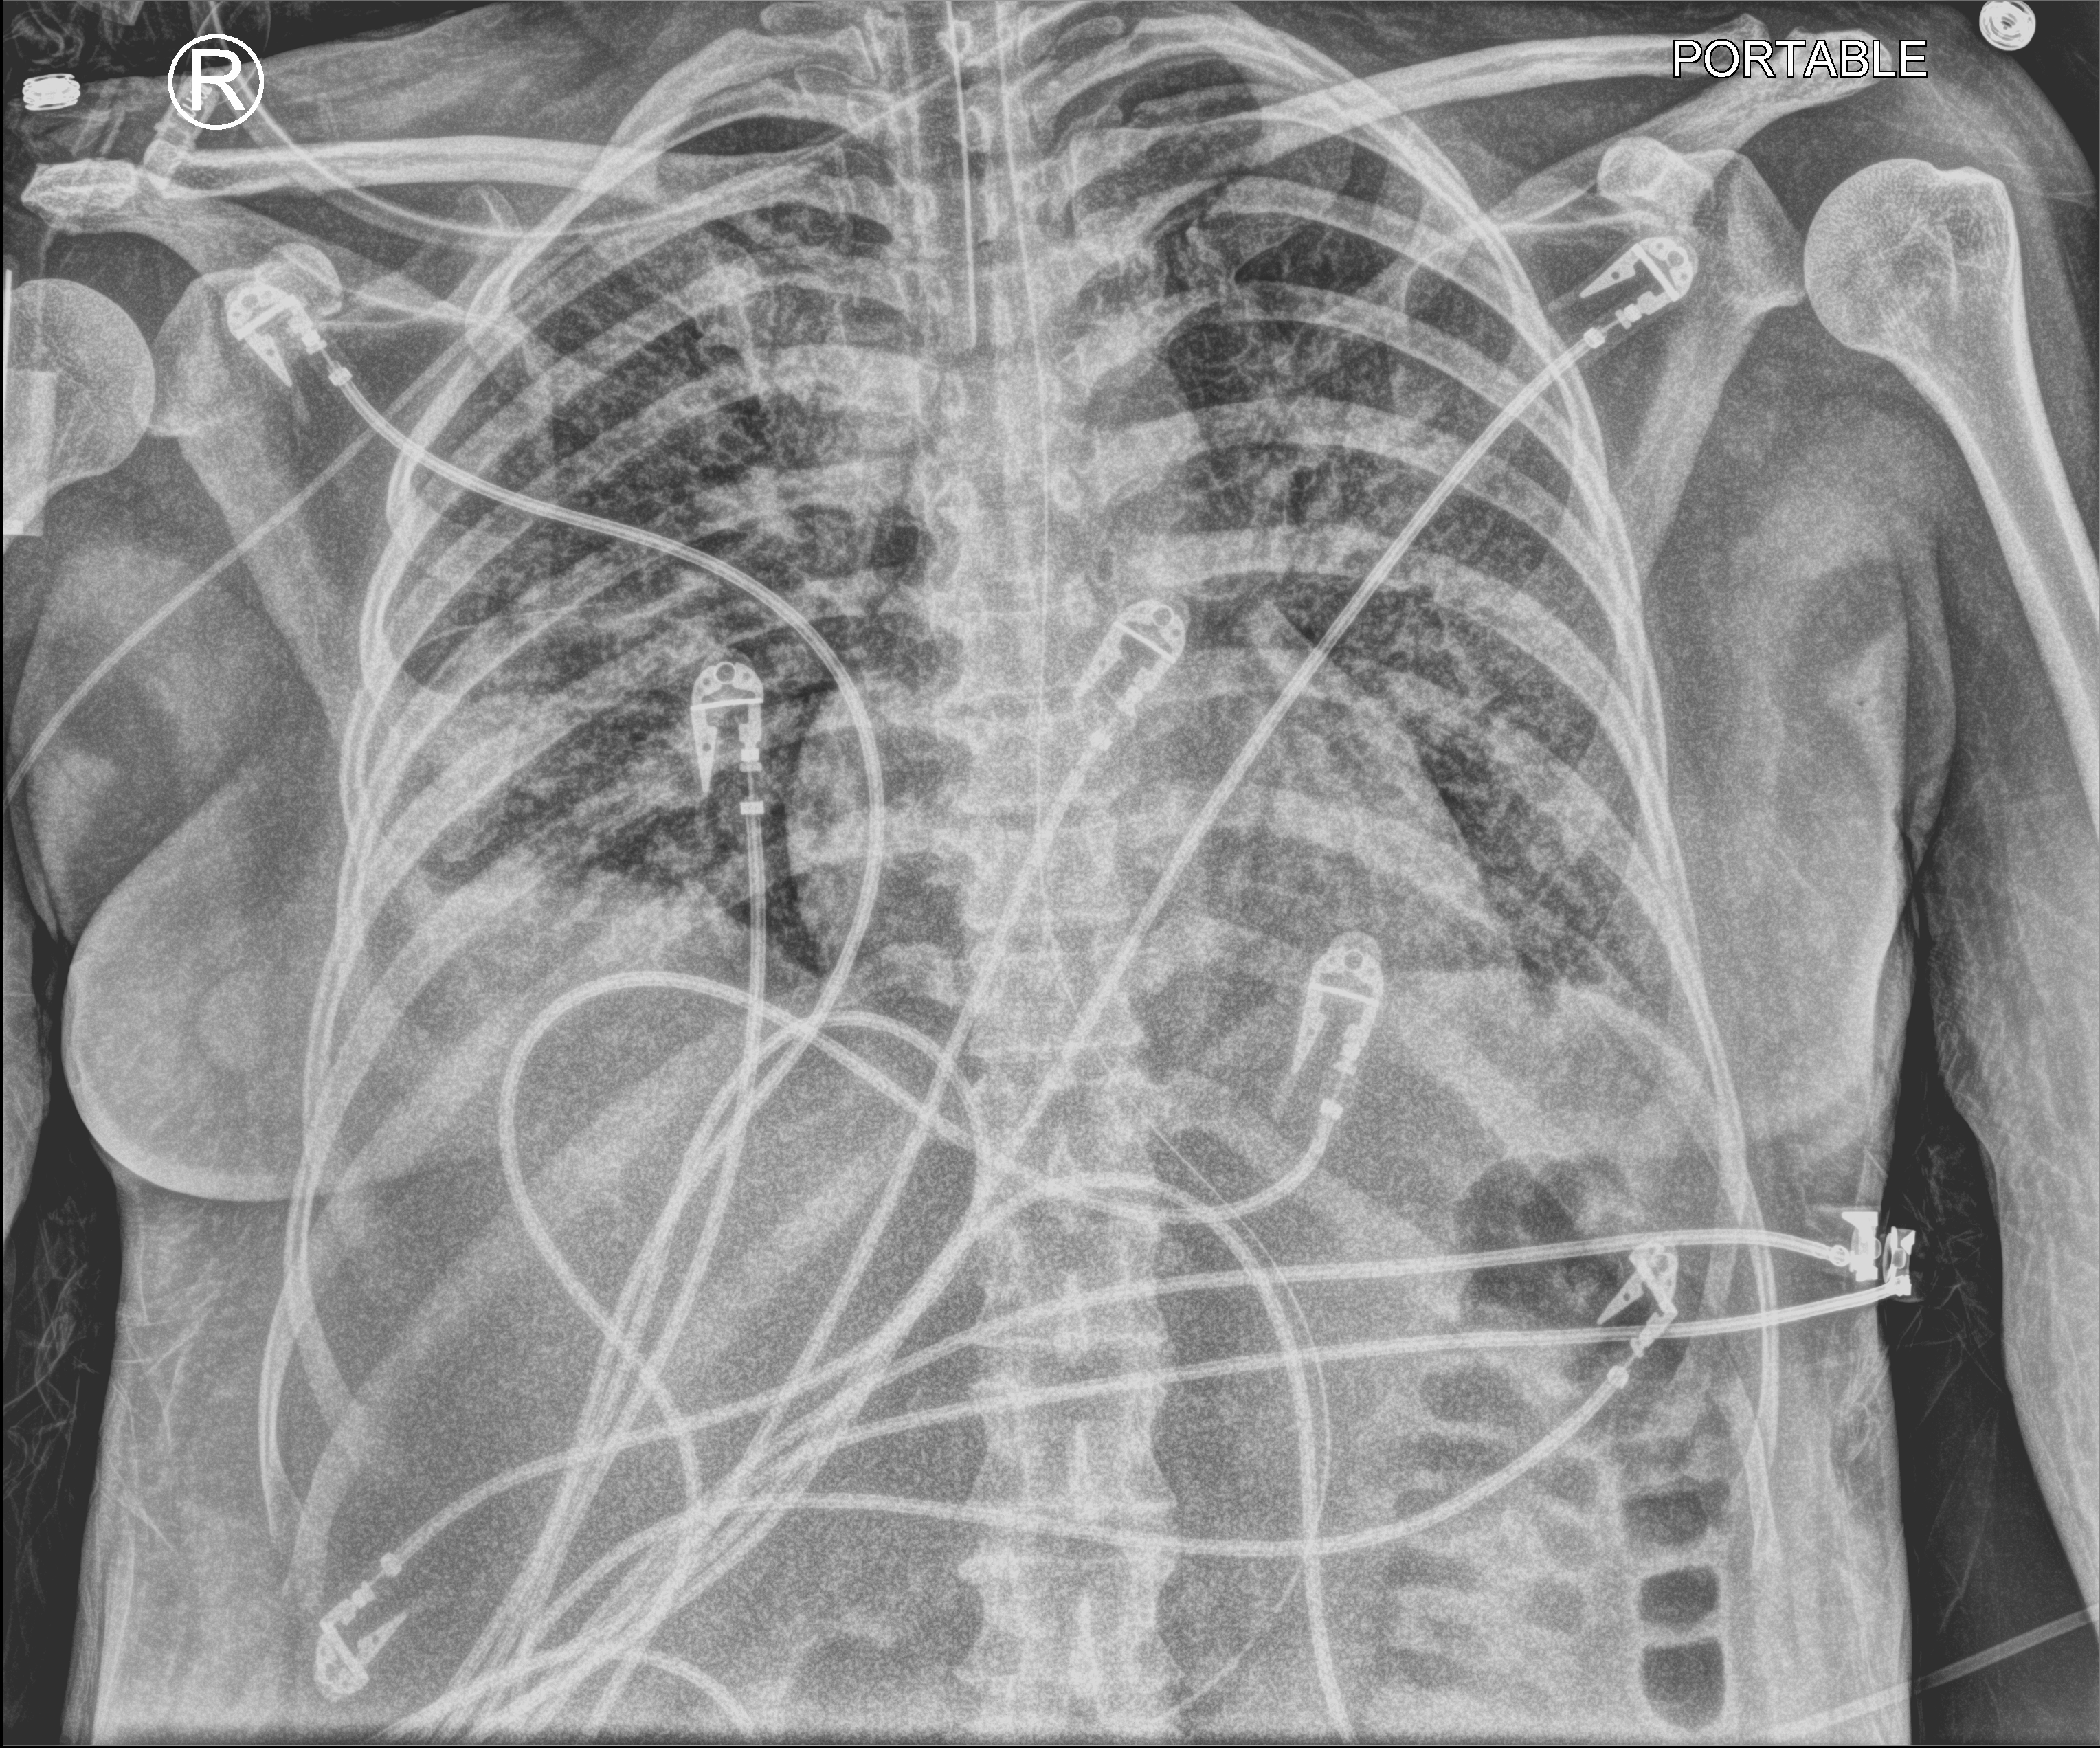
Portable chest radiograph, anteroposterior (AP) projection. Patient hospitalised with COVID-19; female, aged 18–59 years.
Admission-level facts for this patient (not findings on this image; timing relative to this image not recorded):
- mechanically ventilated during this hospital stay: yes
- length of hospital stay: 71 days
- admitted to intensive care during this hospital stay: yes